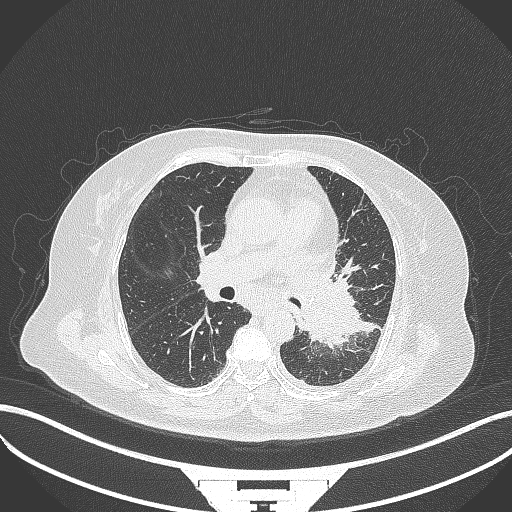
Chest CT, one axial slice. Slice 192 of 322 in the series (ordered by position). 120 kVp. Lung window (W 1500 / L -600 HU). 1 mm slice thickness. 512 × 512 image matrix, field of view 400 × 400 mm. Female patient, age 69 years. Case-level facts recorded for this patient, not image findings: clinical TNM (as recorded): T2b N3 M1.
Structures marked on this image (bounding box drawn by a radiologist):
- lung tumour (recorded histology: adenocarcinoma): box from (x=301, y=278) to (x=365, y=350) px